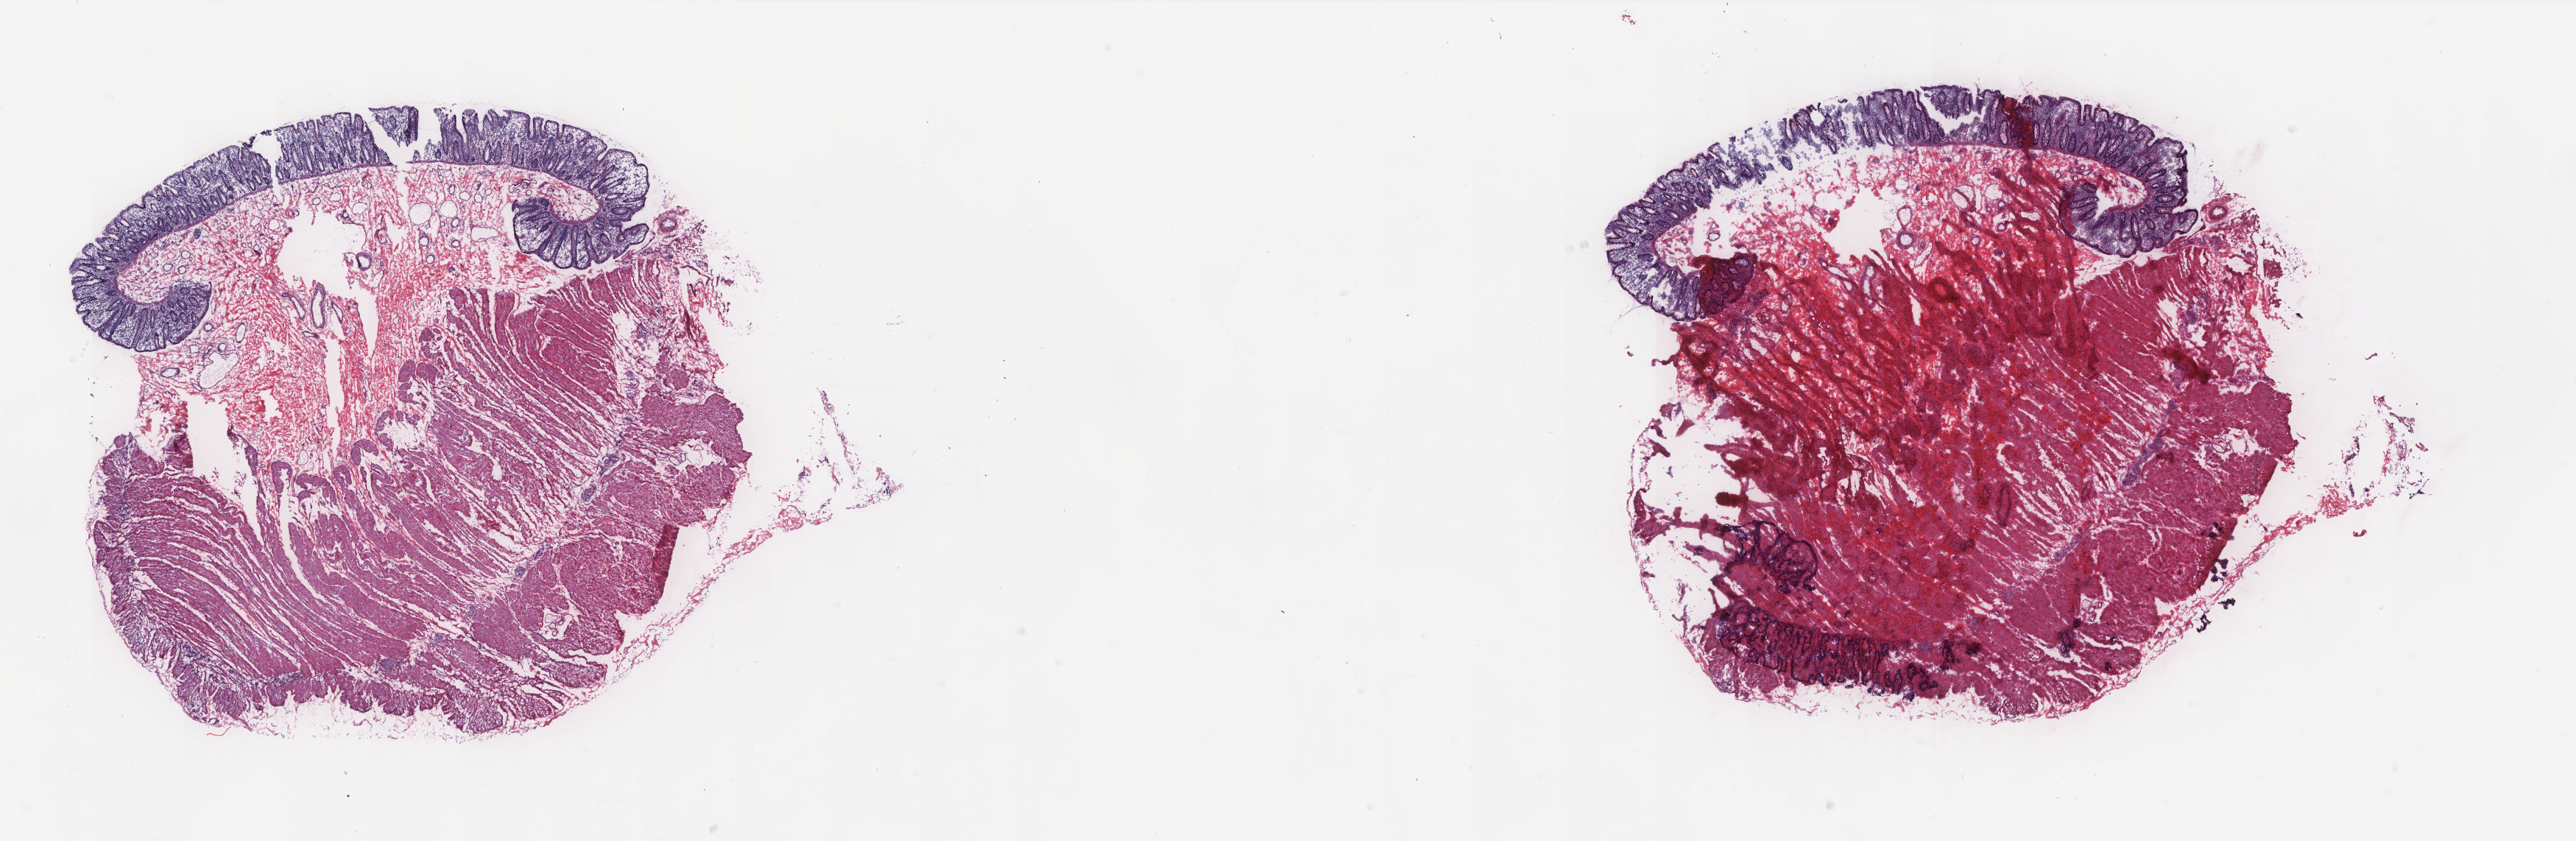
H&E whole-slide image — a low-resolution overview of the entire scanned area, about 27.9 x 9.1 mm (slide scanned at 20x); frozen section from the bottom of the tissue portion; sample: solid tissue normal (non-tumour tissue), colon. Female patient. Pathologist review of this section (percent, as recorded): tumour cells 0%, normal cells 100%. Infiltration values recorded for this section: lymphocyte infiltration 35%, monocyte infiltration 8%, neutrophil infiltration 0%.
This section: solid tissue normal (non-tumour) sample from the same patient. Patient diagnosis: Mucinous adenocarcinoma (cecum).